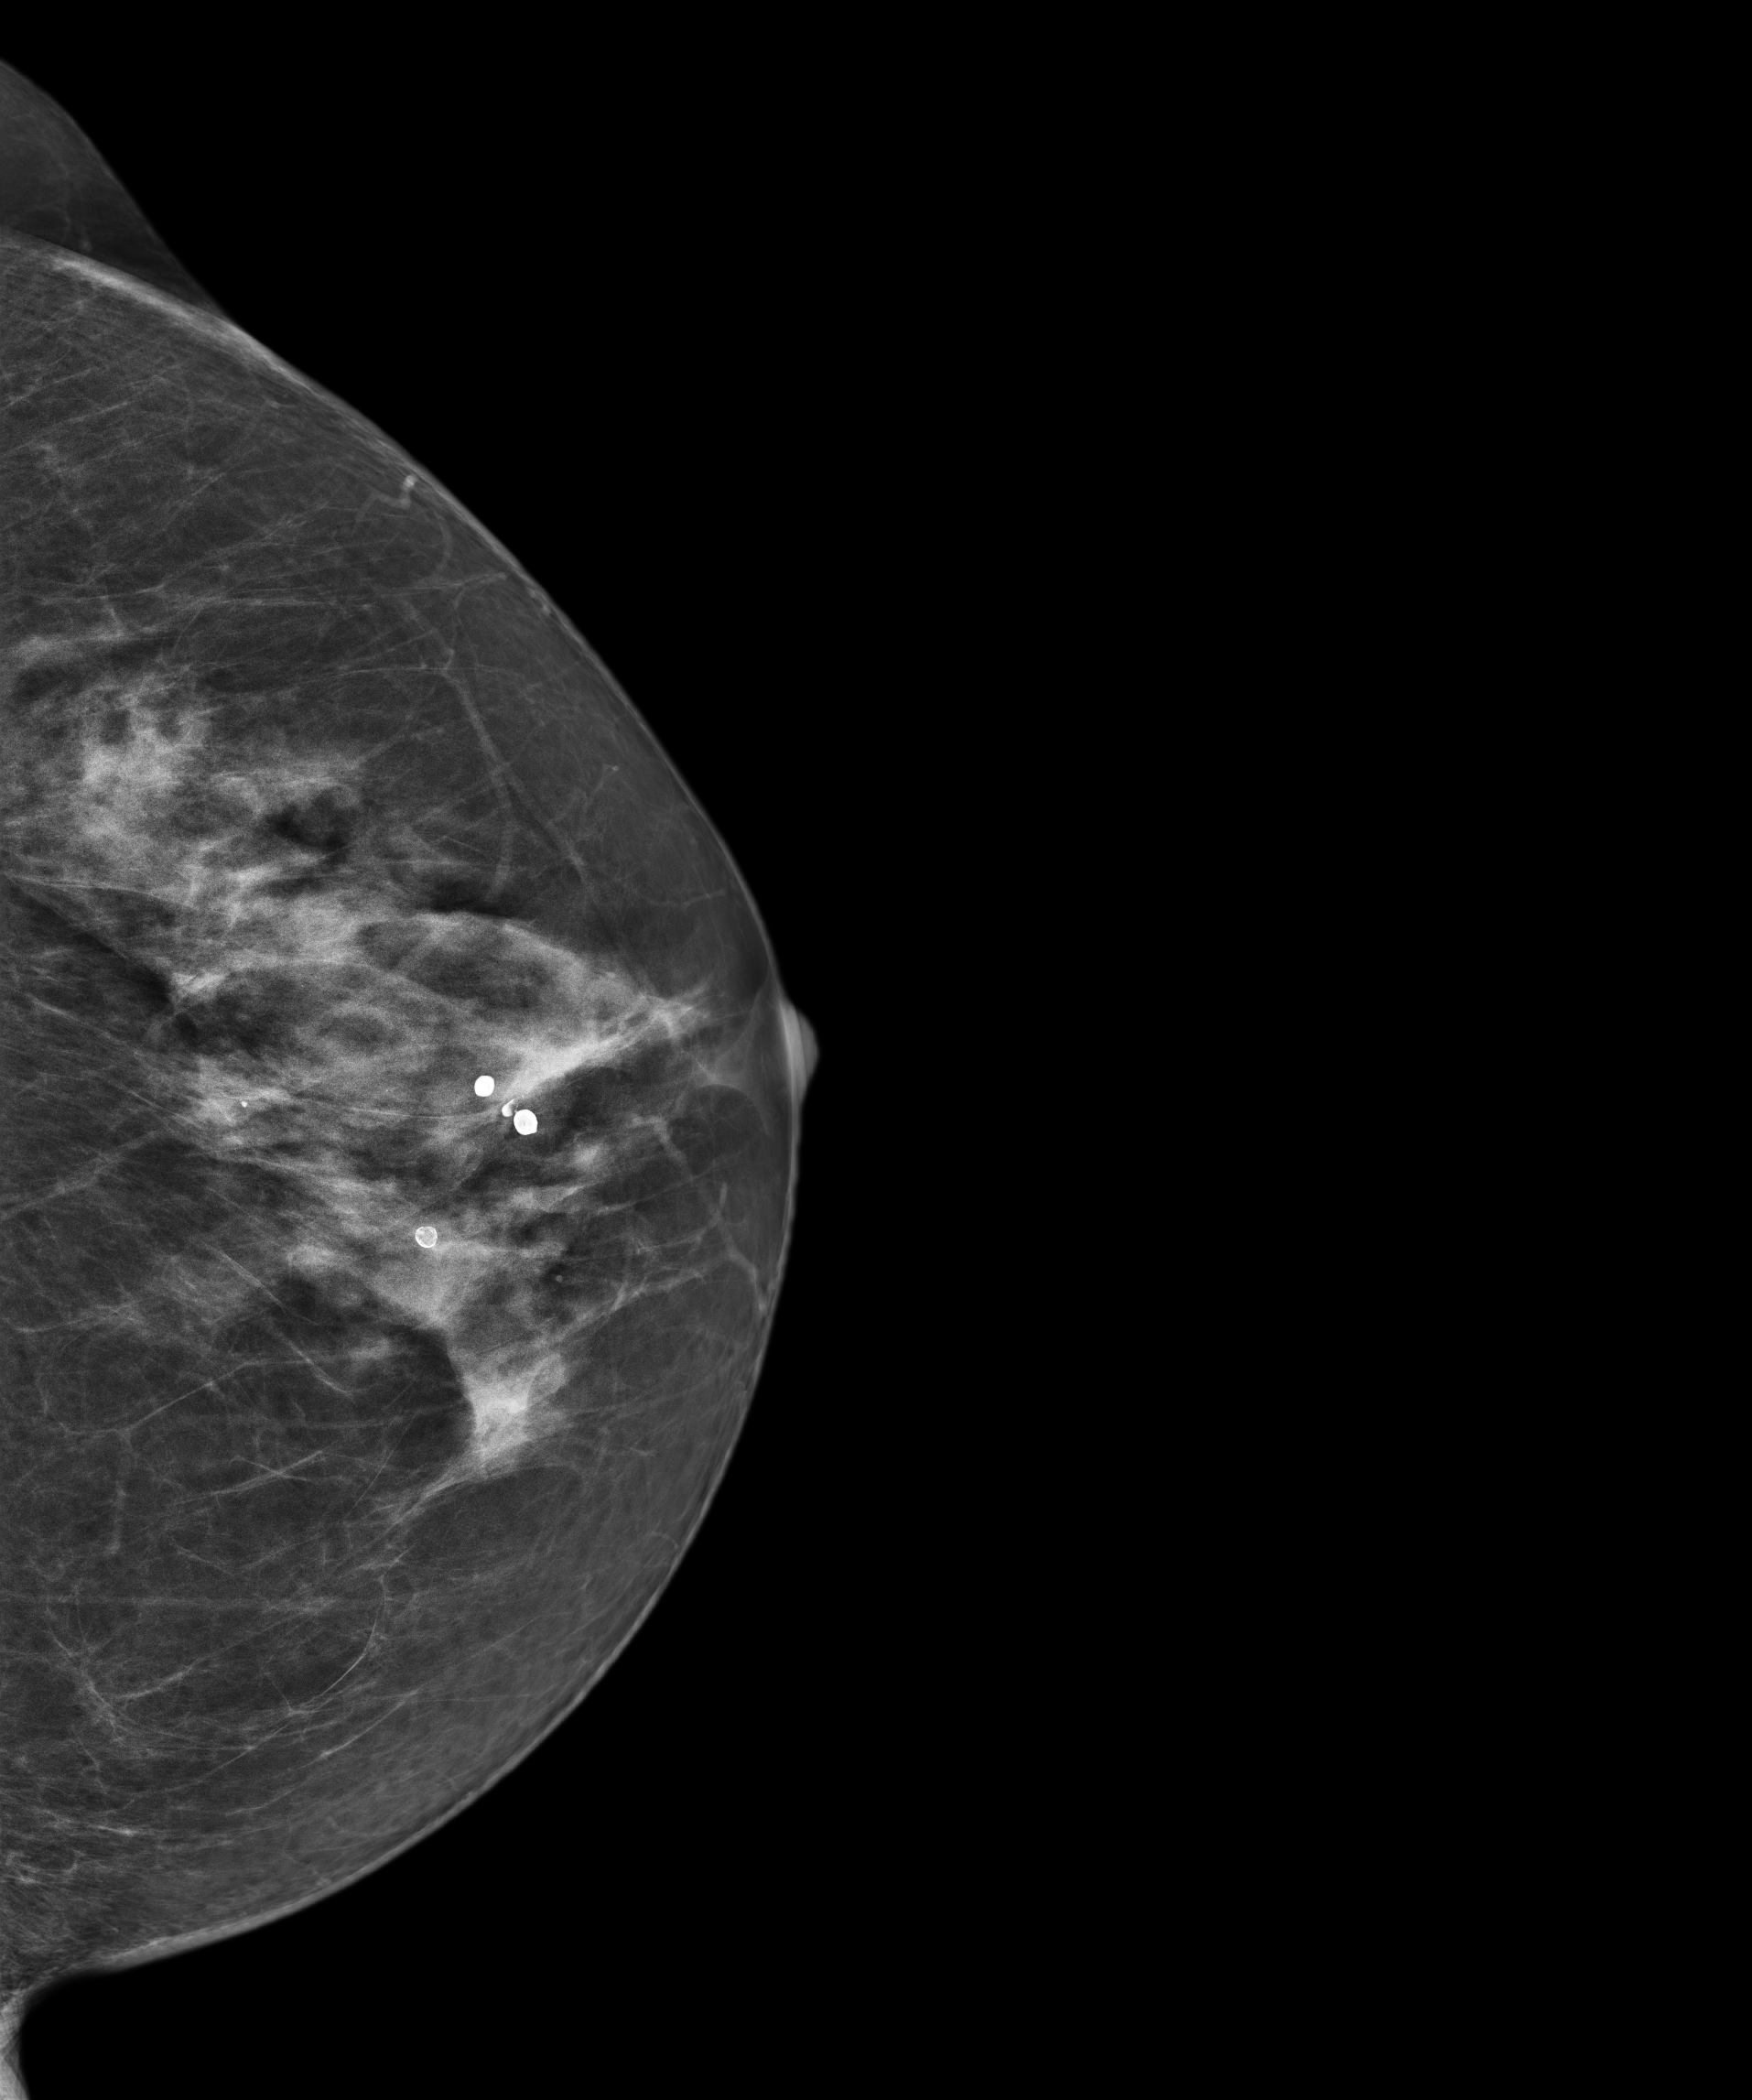
Screening examination.
Image type: full-field digital mammogram. Breast: left. Projection: CC view.